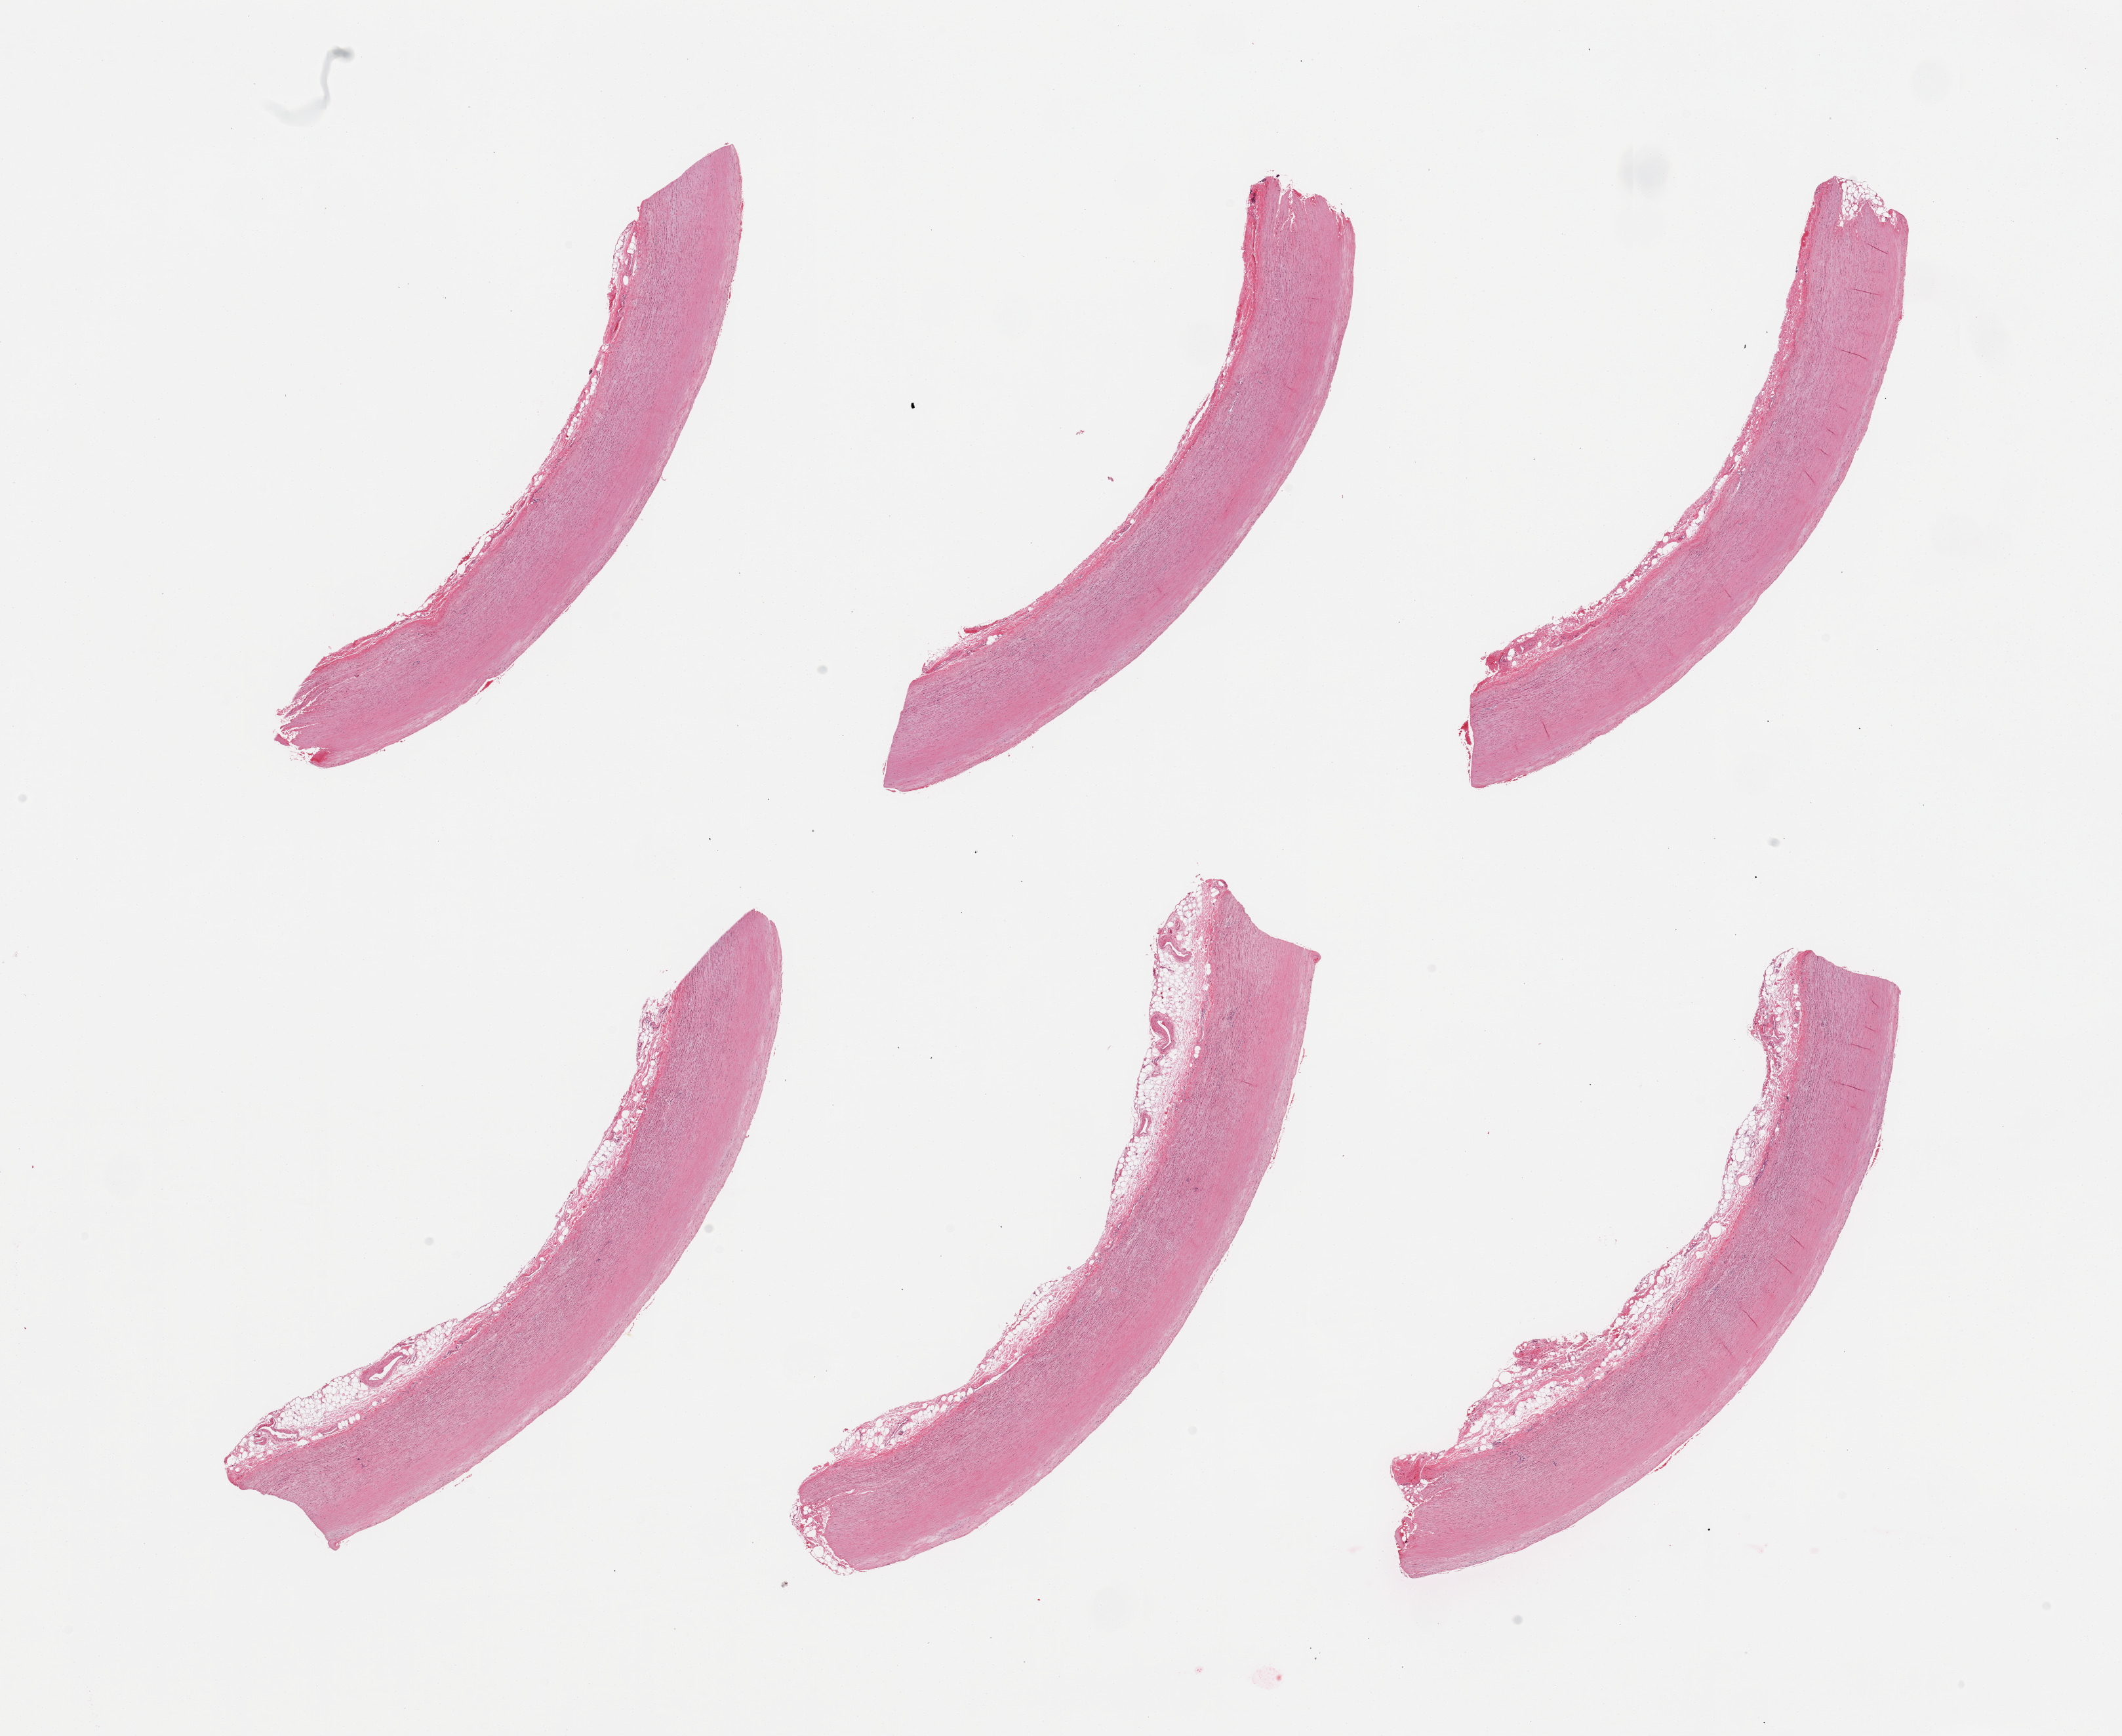
Digitized haematoxylin and eosin-stained section, brightfield, whole scanned area (about 25.6 x 20.9 mm, acquisition: 20x scan) shown as a low-resolution overview; PAXgene-fixed, paraffin-embedded tissue; target tissue: aorta; donor tissue sample. Donor sex: male.
- pathologist's review note for this sample: 6 pieces; flat plaques; fatty adventitia on 3 pieces